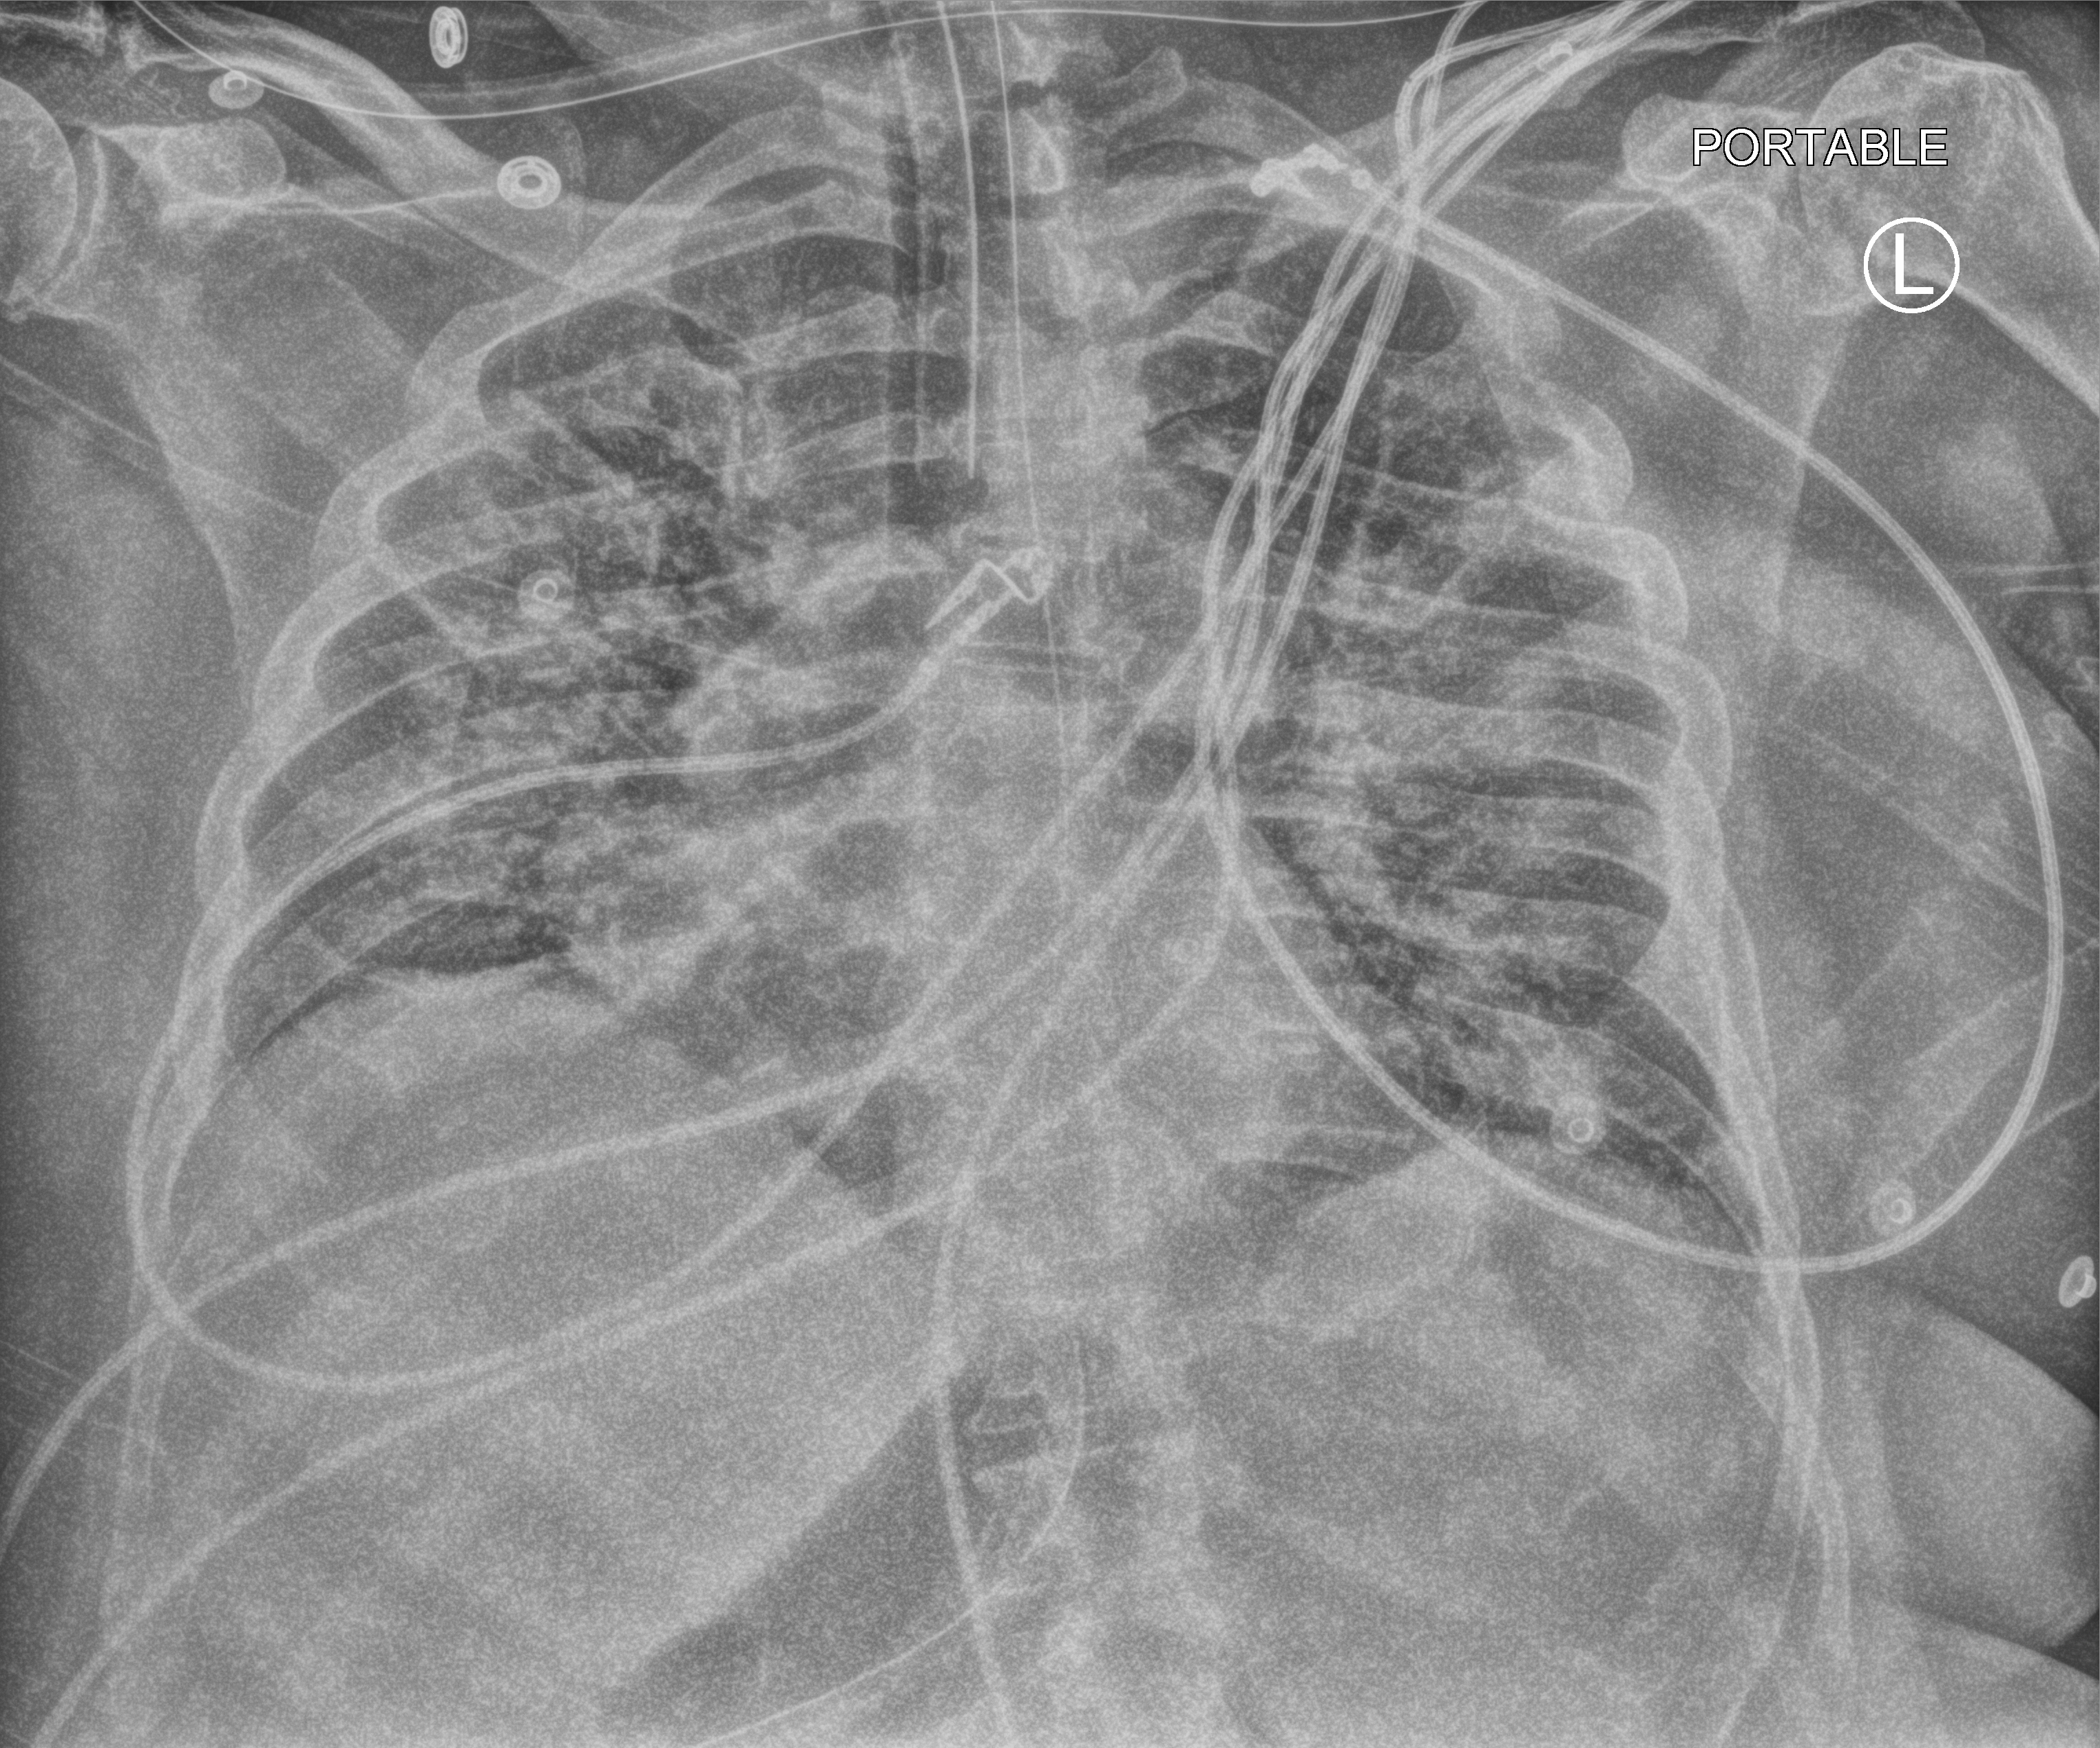
Bedside chest radiograph (computed radiography); anteroposterior (AP) projection. Patient hospitalised with COVID-19; male, aged 18–59 years.
Hospital-stay facts (about this admission, not read from this image; timing relative to this image not recorded): mechanically ventilated during this hospital stay: yes.